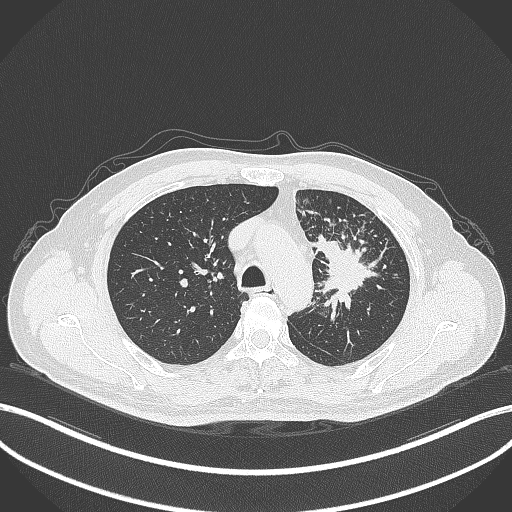
Chest CT, one axial slice. Slice 263 of 386 in the series (ordered by position). Reconstruction kernel B70f. 120 kVp. Lung window (W 1500 / L -600 HU). 1 mm slice thickness. 512 × 512 image matrix, field of view 400 × 400 mm. Male patient, age 69 years. From the clinical record (not read from this slice): clinical TNM (as recorded): T2a N2 M0; histopathological grade: G2-3.
Annotated regions visible in this slice (bounding box drawn by a radiologist):
- lung tumour (recorded histology: adenocarcinoma): bounding box (x1, y1, x2, y2) in pixels: (311, 232, 383, 317)